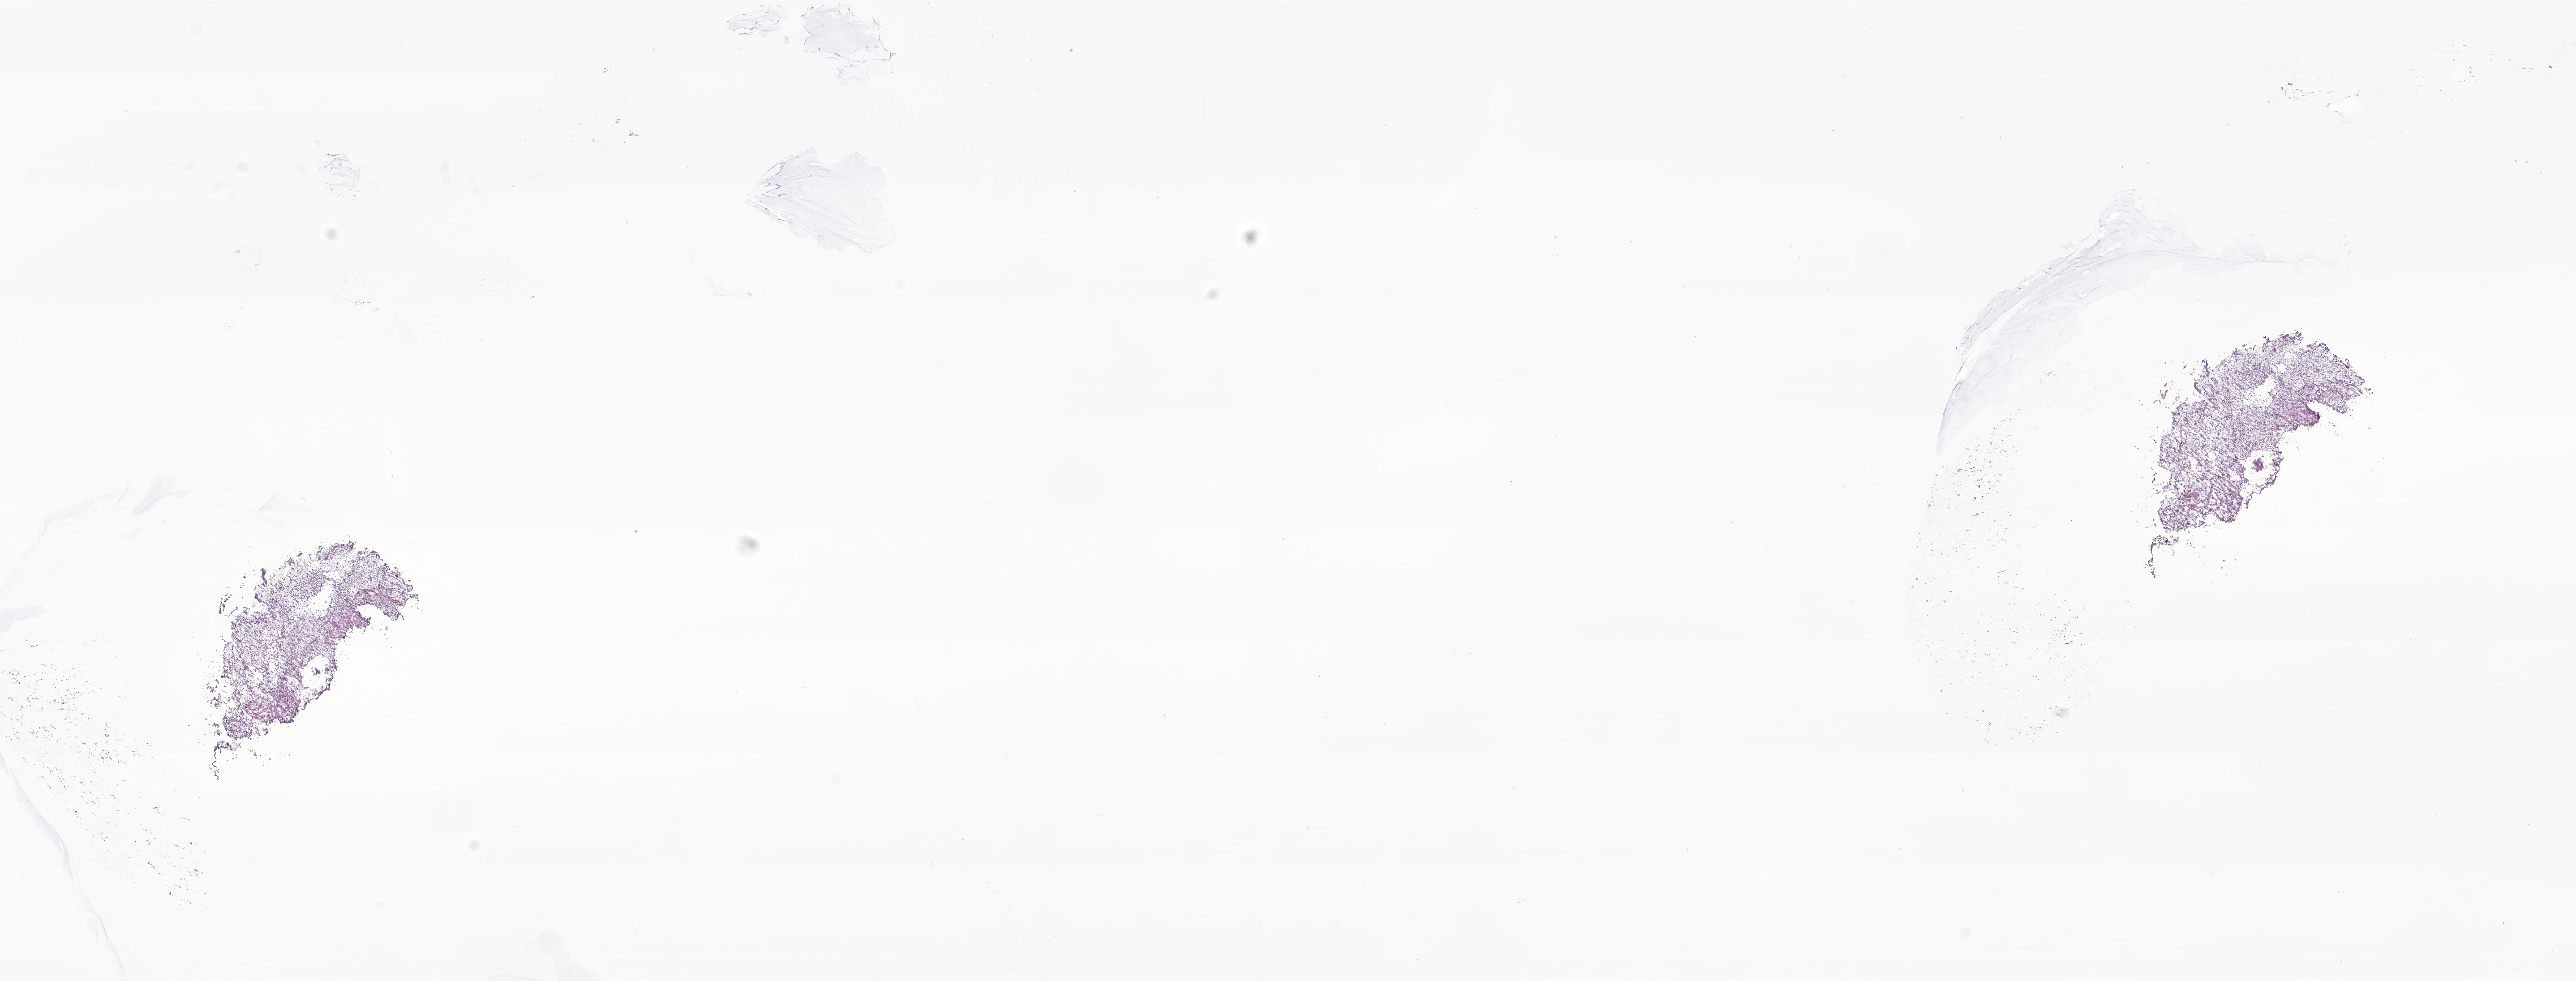
Digitized H&E-stained section of tumor tissue from the brain stem, a low-resolution overview of the entire scanned area, about 24.2 x 9.2 mm. Frozen section (OCT-embedded). Patient male; age 135 months (11 years 3 months).
Diagnosis: Medulloblastoma, NOS.